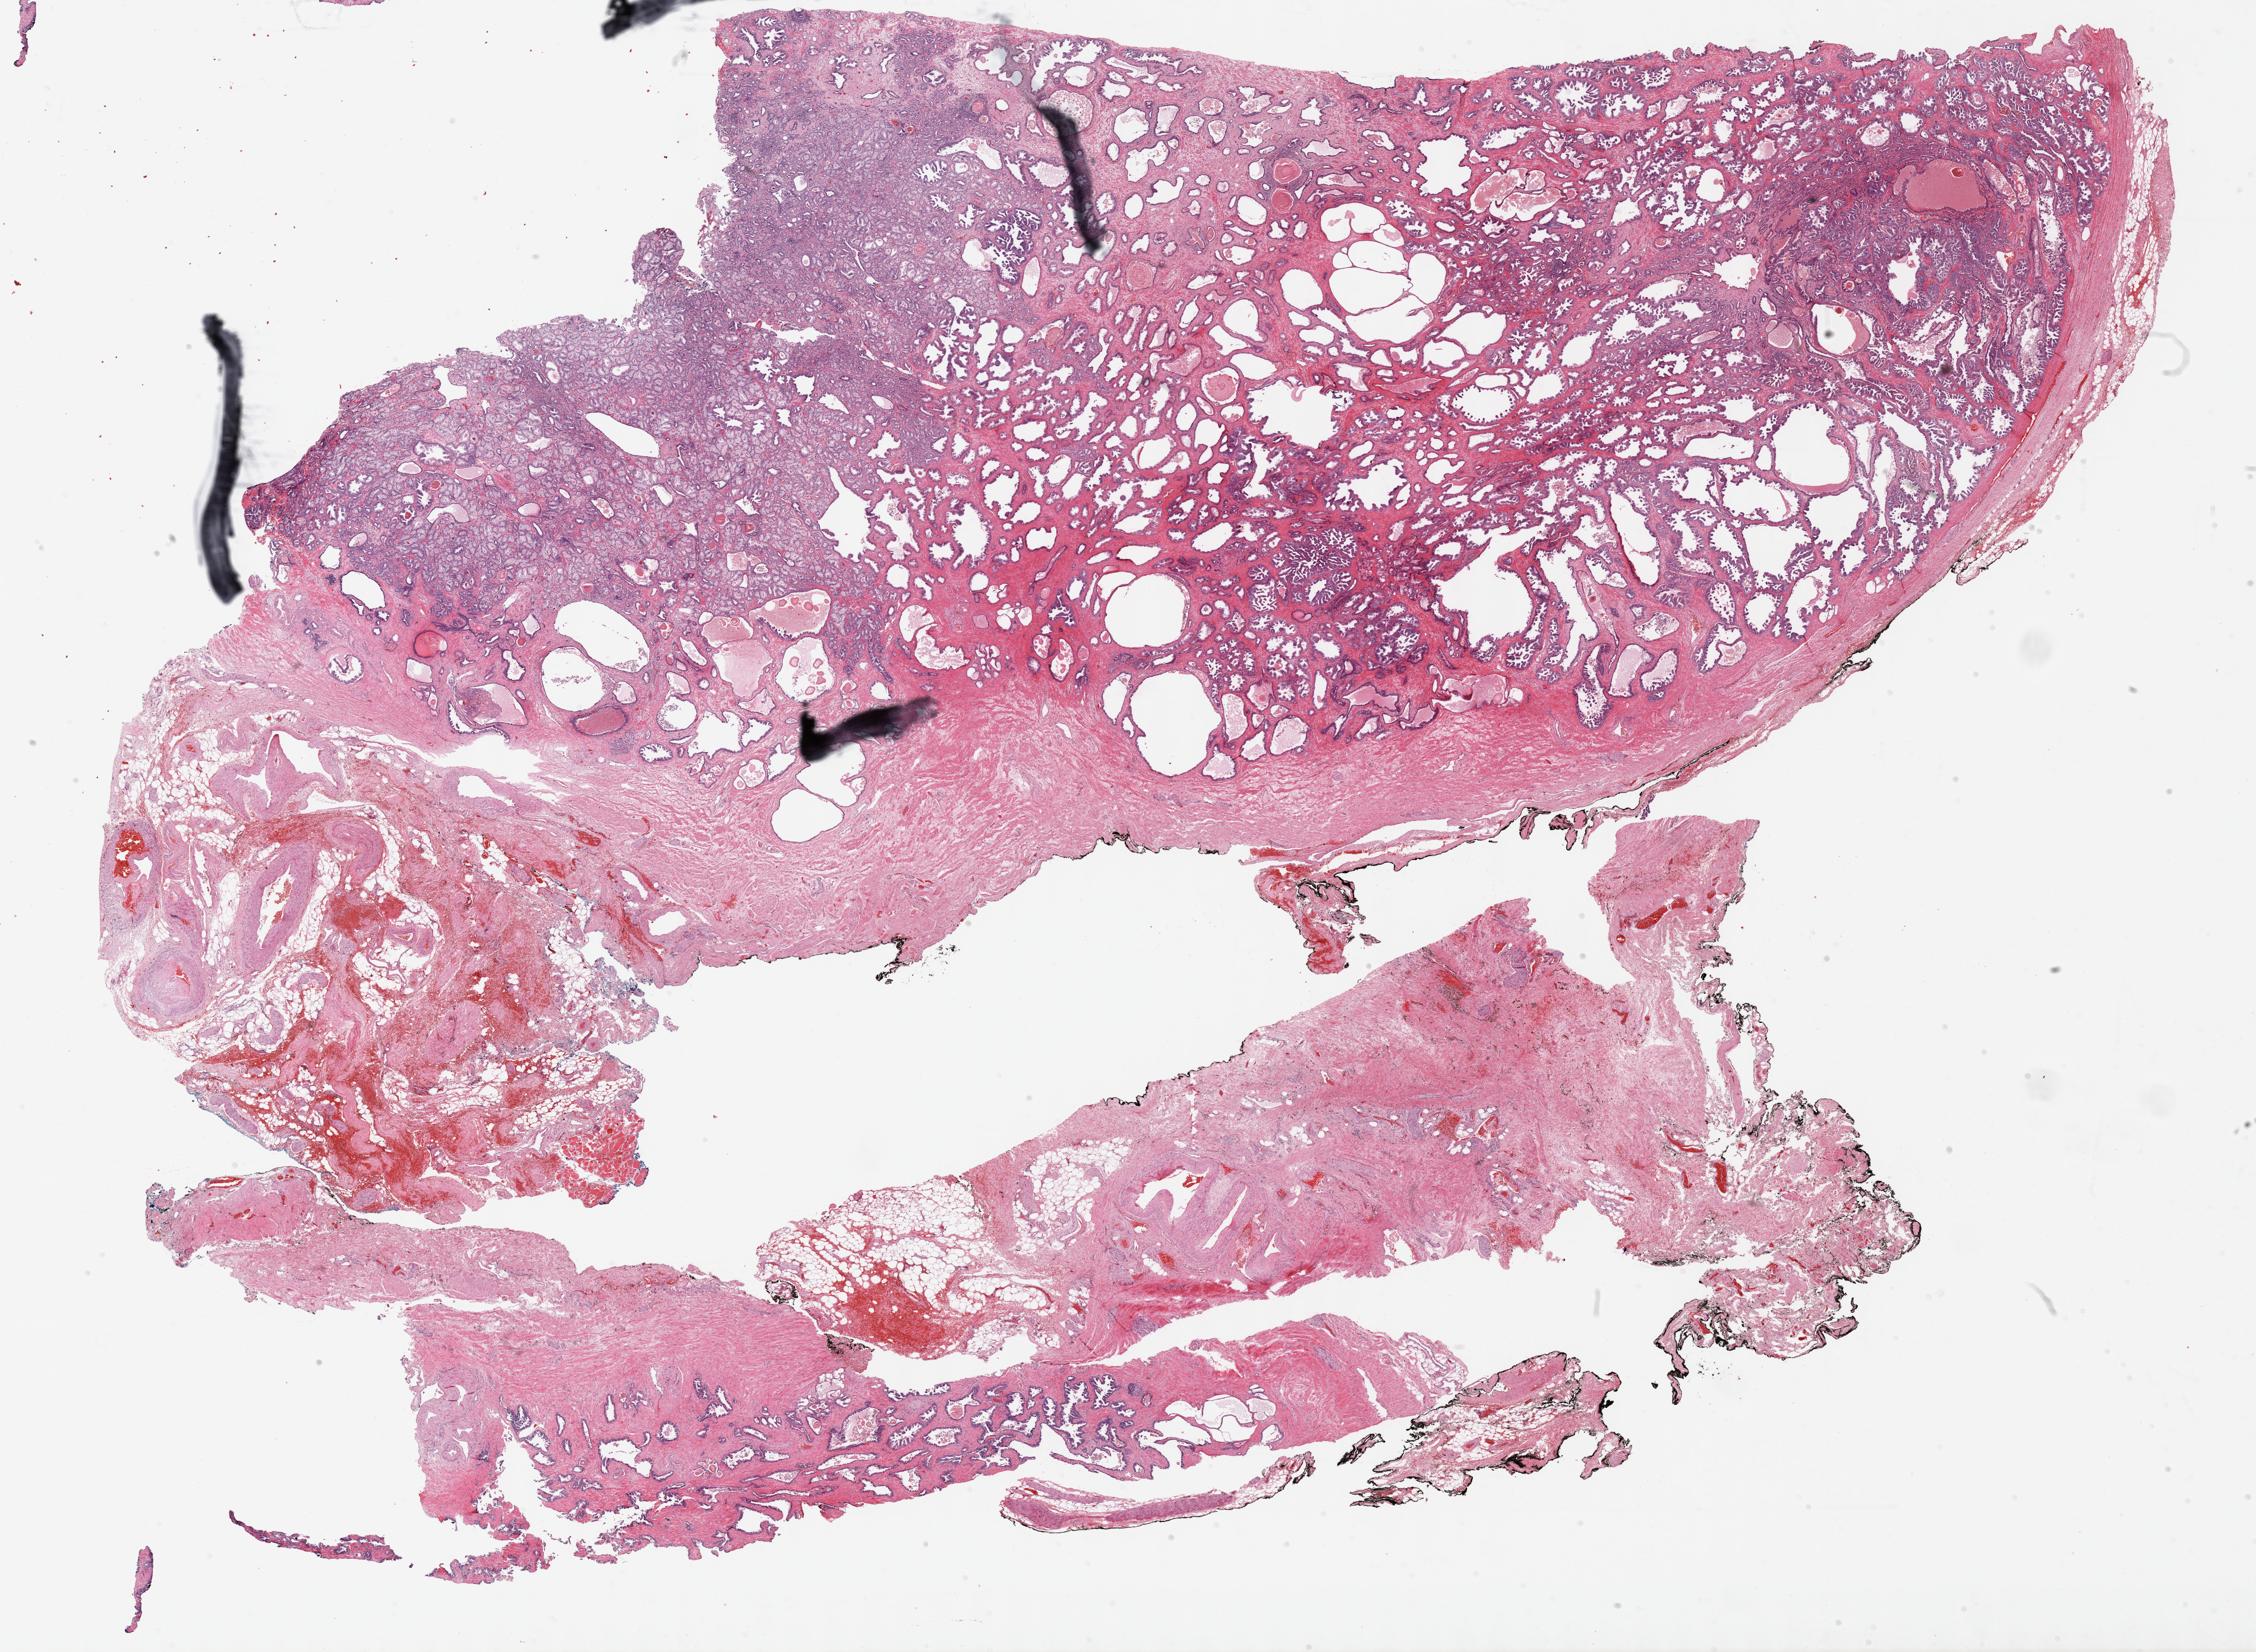
H&E-stained whole-slide image, shown as a low-resolution overview of the whole scanned area (about 30.7 x 22.5 mm, acquisition: 40x scan); formalin-fixed paraffin-embedded (FFPE) diagnostic section; prostate, primary tumour sample. Male patient; age at initial diagnosis 57 years. Gleason score: 7 (3+4).
* pathologic diagnosis: Adenocarcinoma, NOS (prostate gland)